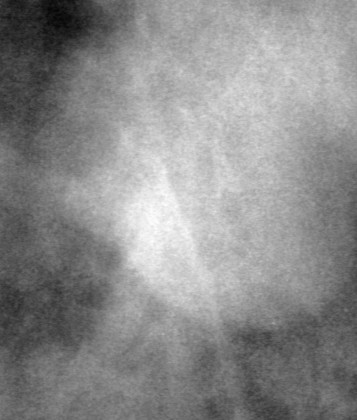
Cropped region of a digitized screen-film mammogram centred on a radiologist-marked abnormality, left breast, CC view, BI-RADS breast density category 3 (scale 1–4).
Finding: mass, shape lobulated, margins circumscribed; BI-RADS assessment category 0 (incomplete: needs additional imaging); pathology result (as recorded, not read from the image): benign.